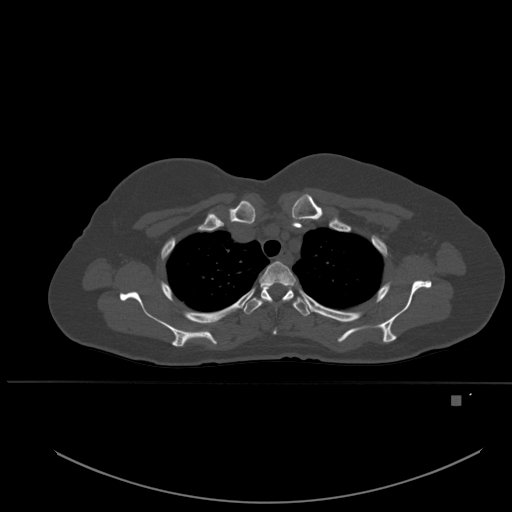
CT including the spine, one axial slice. Position 399 of 651 along the scan axis. Bone window (W 1800 / L 400 HU). 512 × 512 image matrix. Female patient, age 49 years. From the clinical record (not read from this slice): primary cancer: breast; vertebrae with lytic lesions (as recorded): L3, T12, L4.
Annotated regions visible in this slice (semi-automatic segmentation, software-assisted and operator-edited):
- T2 vertebra: bounding box [x1, y1, x2, y2] px = [259, 261, 296, 334]
- T3 vertebra: [243, 285, 310, 316]